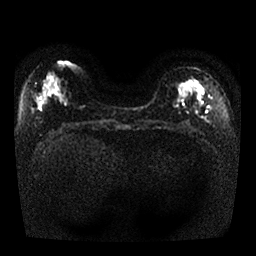
Breast MRI, one axial slice. Slice 11 of 25 in the series (ordered by position). Diffusion-weighted series; image 2 of 4 stored at this slice position (different b-values; order by instance number). 1.5 T. 4 mm slice thickness. 256 × 256 image matrix, field of view 330 × 330 mm. Female patient.
Annotated regions visible in this slice (manually delineated by an expert):
- tumour on diffusion-weighted imaging: bounding box [x1, y1, x2, y2] px = [184, 80, 201, 90]